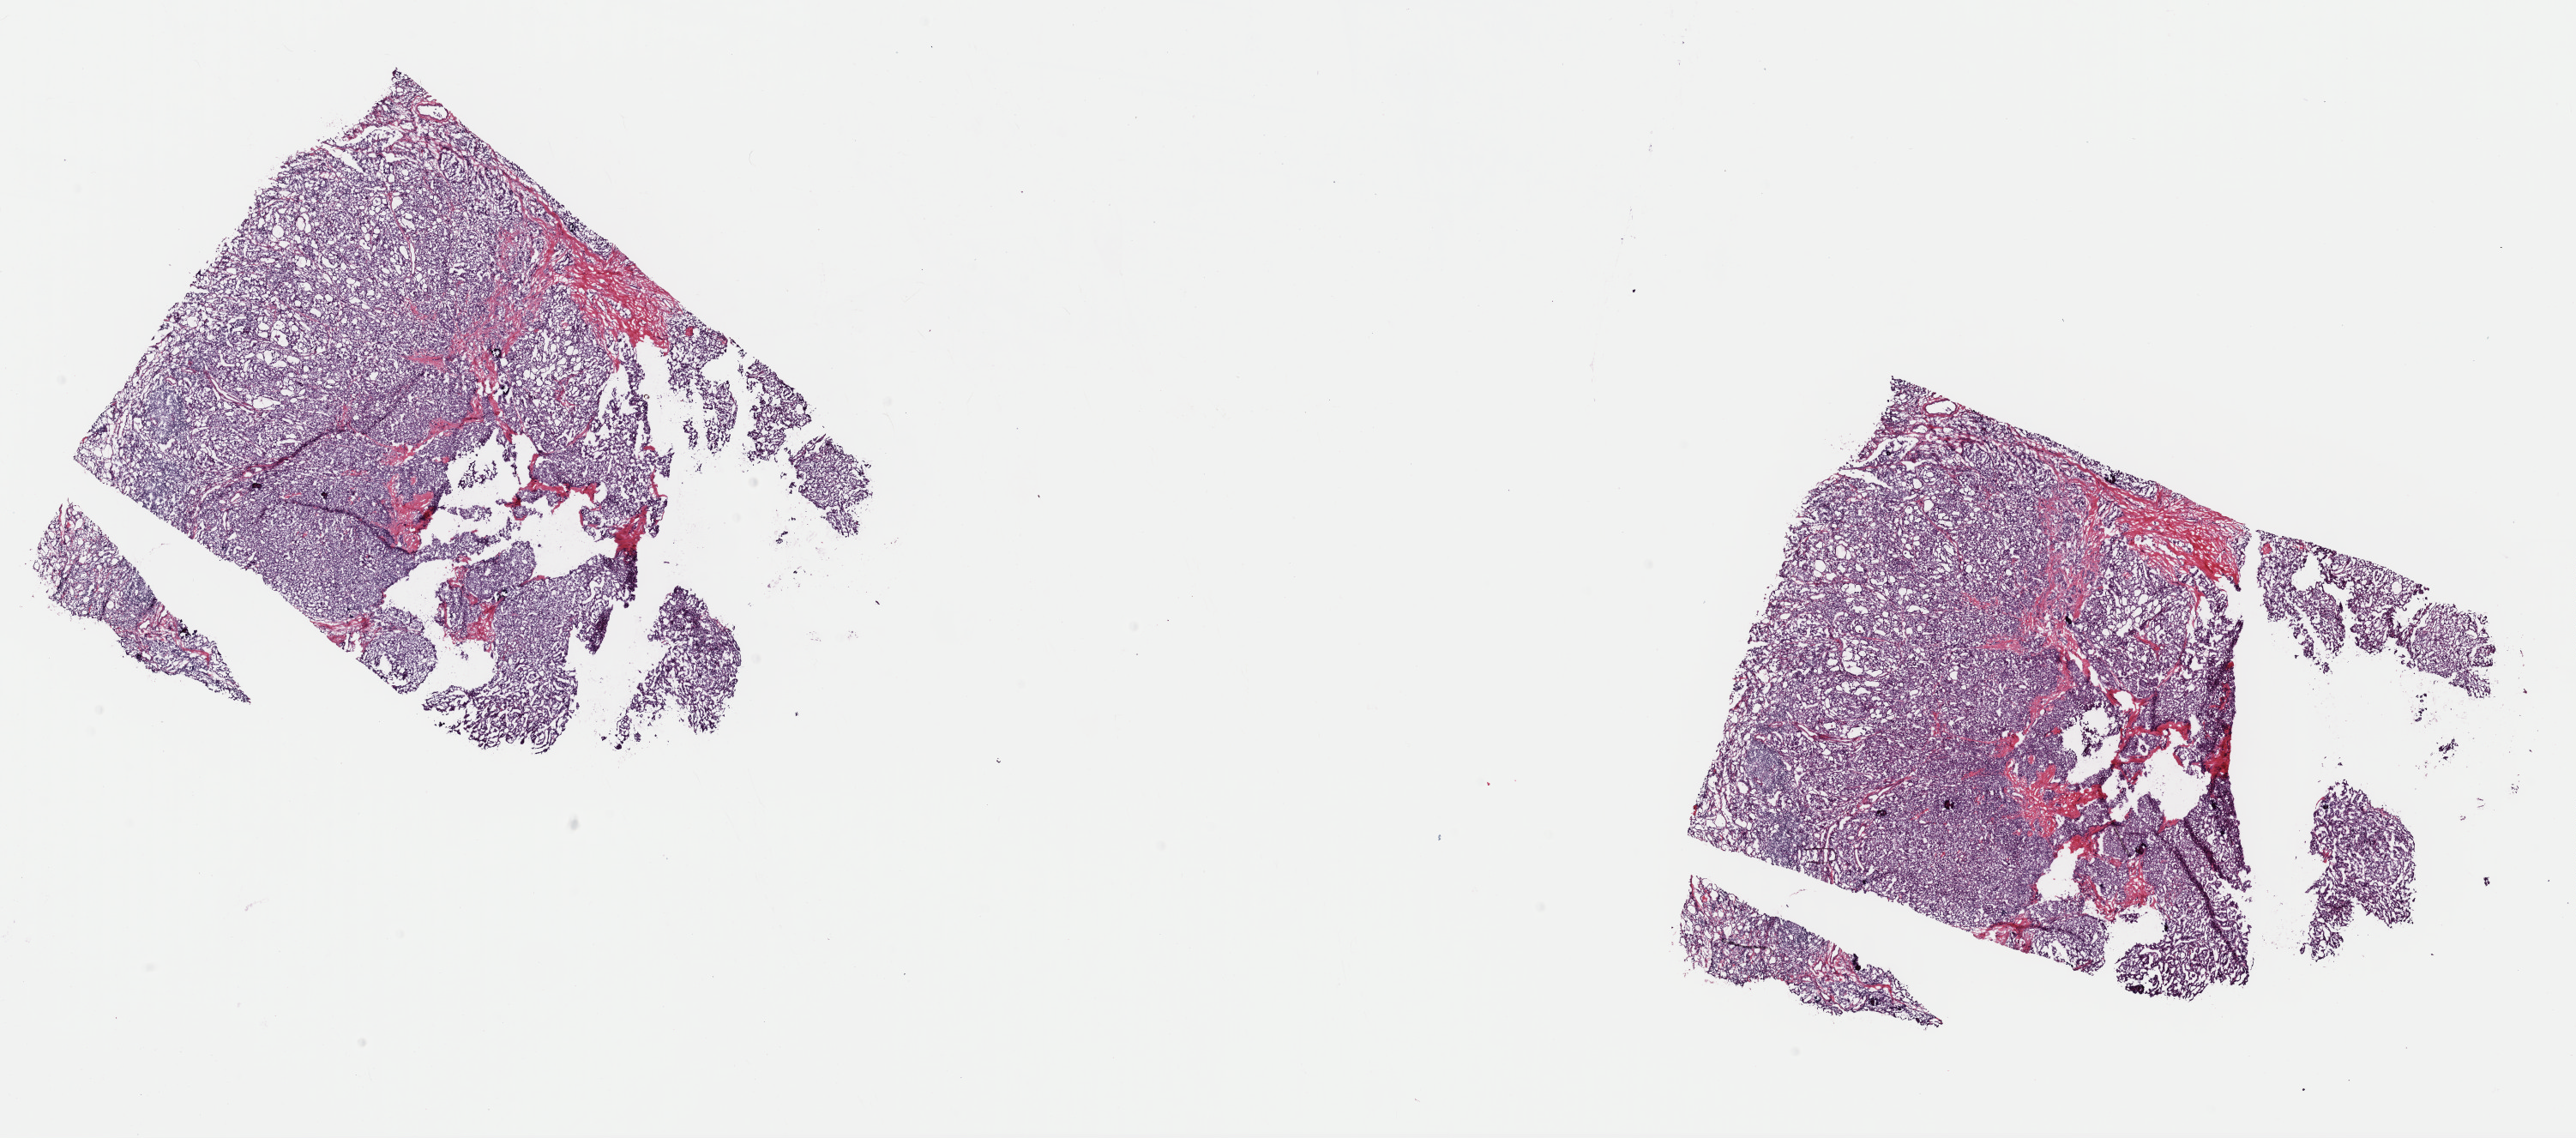
Digitized Hematoxylin and eosin (H&E) stained tissue section (whole slide) — whole scanned area (about 23.7 x 10.5 mm) shown as a low-resolution overview, frozen section from the top of the tissue portion, thyroid, primary tumour sample. Patient: female, age at initial diagnosis 23 years. Slide review estimates, as recorded: tumour cells 90%, tumour nuclei 90%, normal cells 0%, stromal cells 10%, necrosis 0%. Inflammatory infiltration, as recorded: lymphocyte infiltration 30%, monocyte infiltration 0%, neutrophil infiltration 0%.
Histologic diagnosis: Papillary adenocarcinoma, NOS (thyroid gland). AJCC pathologic stage: I (7th edition).